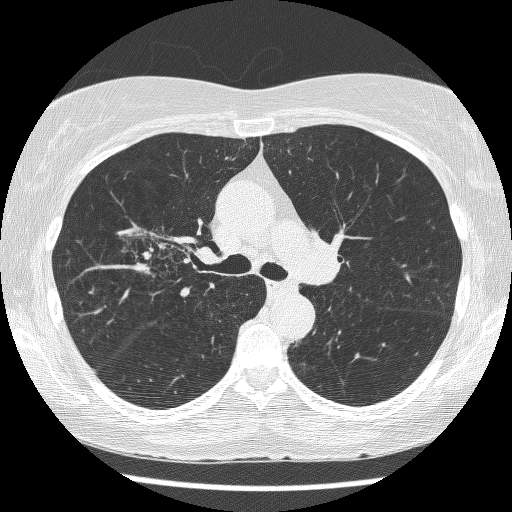
Chest CT (low-dose screening protocol), one axial image, first (baseline) screen, lung window (W 1500 / L -600 HU), 512 × 512 image matrix. Female, age 64 years at enrolment.
Lesion marked by an expert reader, box from (x=125, y=223) to (x=205, y=295) px. The screening reader recorded 3 non-calcified nodules or masses ≥4 mm on this exam; which of them this box marks is not recorded. Official screen result: positive, change unspecified: nodule(s) >= 4 mm or enlarging nodule(s), mass(es), or other non-specific abnormalities suspicious for lung cancer. Participant outcome: lung cancer diagnosed 735 days after this screen — adenocarcinoma, NOS, right upper lobe, right middle lobe, right hilum, stage IV (AJCC 6th edition), 85 mm at pathology.